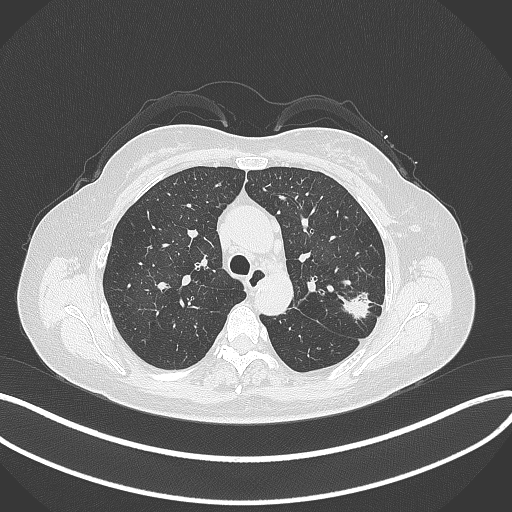
Chest CT, one axial slice; slice 228 of 319 in the series (ordered by position); reconstruction kernel B70f; 120 kVp; lung window (W 1500 / L -600 HU); 1 mm slice thickness; 512 × 512 image matrix, field of view 400 × 400 mm. Patient: female, 60 years. From the clinical record (not read from this slice): clinical TNM (as recorded): T1c N0 M0.
Structures marked on this image (rectangle marked by the reading radiologist):
- lung tumour (recorded histology: adenocarcinoma): bounding box <340,288,376,325> (left, top, right, bottom; pixels)